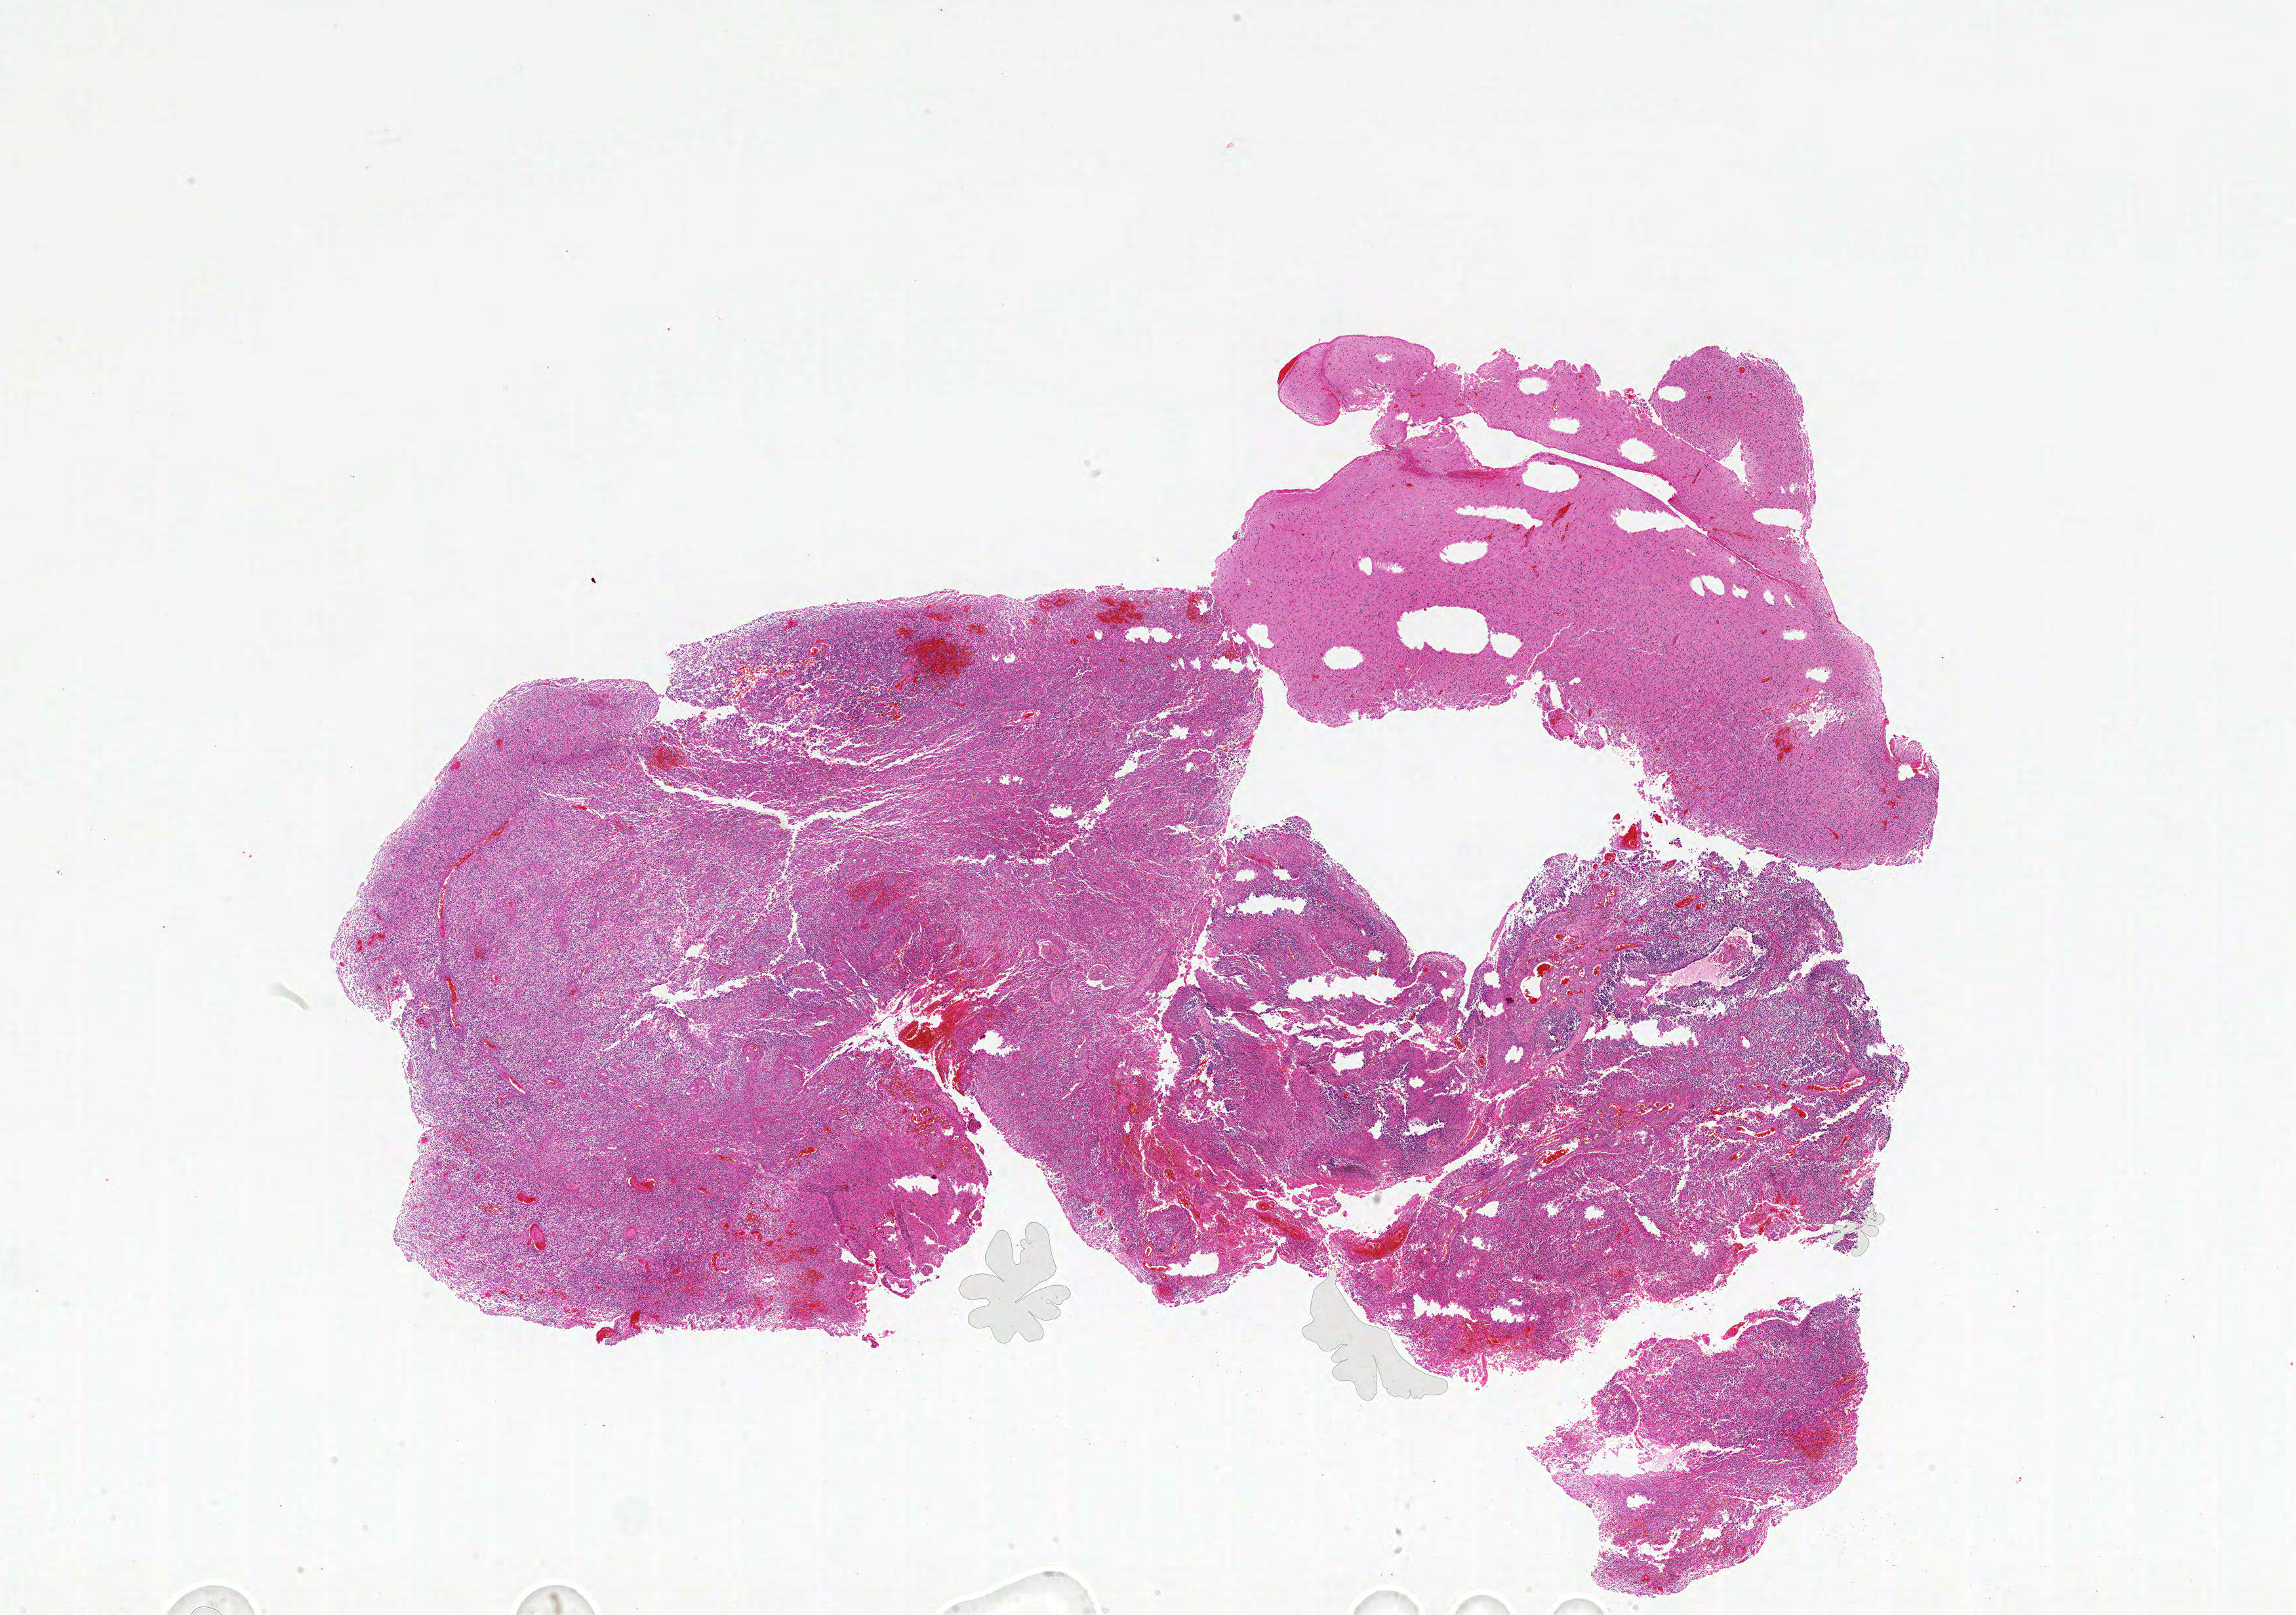
Whole-slide histology image, Hematoxylin and eosin (H&E) stained, low-resolution overview of the scanned area, about 28.0 x 19.7 mm, formalin-fixed paraffin-embedded (FFPE) diagnostic section, brain, primary tumour sample. Male patient; age at initial diagnosis 58 years.
Diagnosis: Glioblastoma.